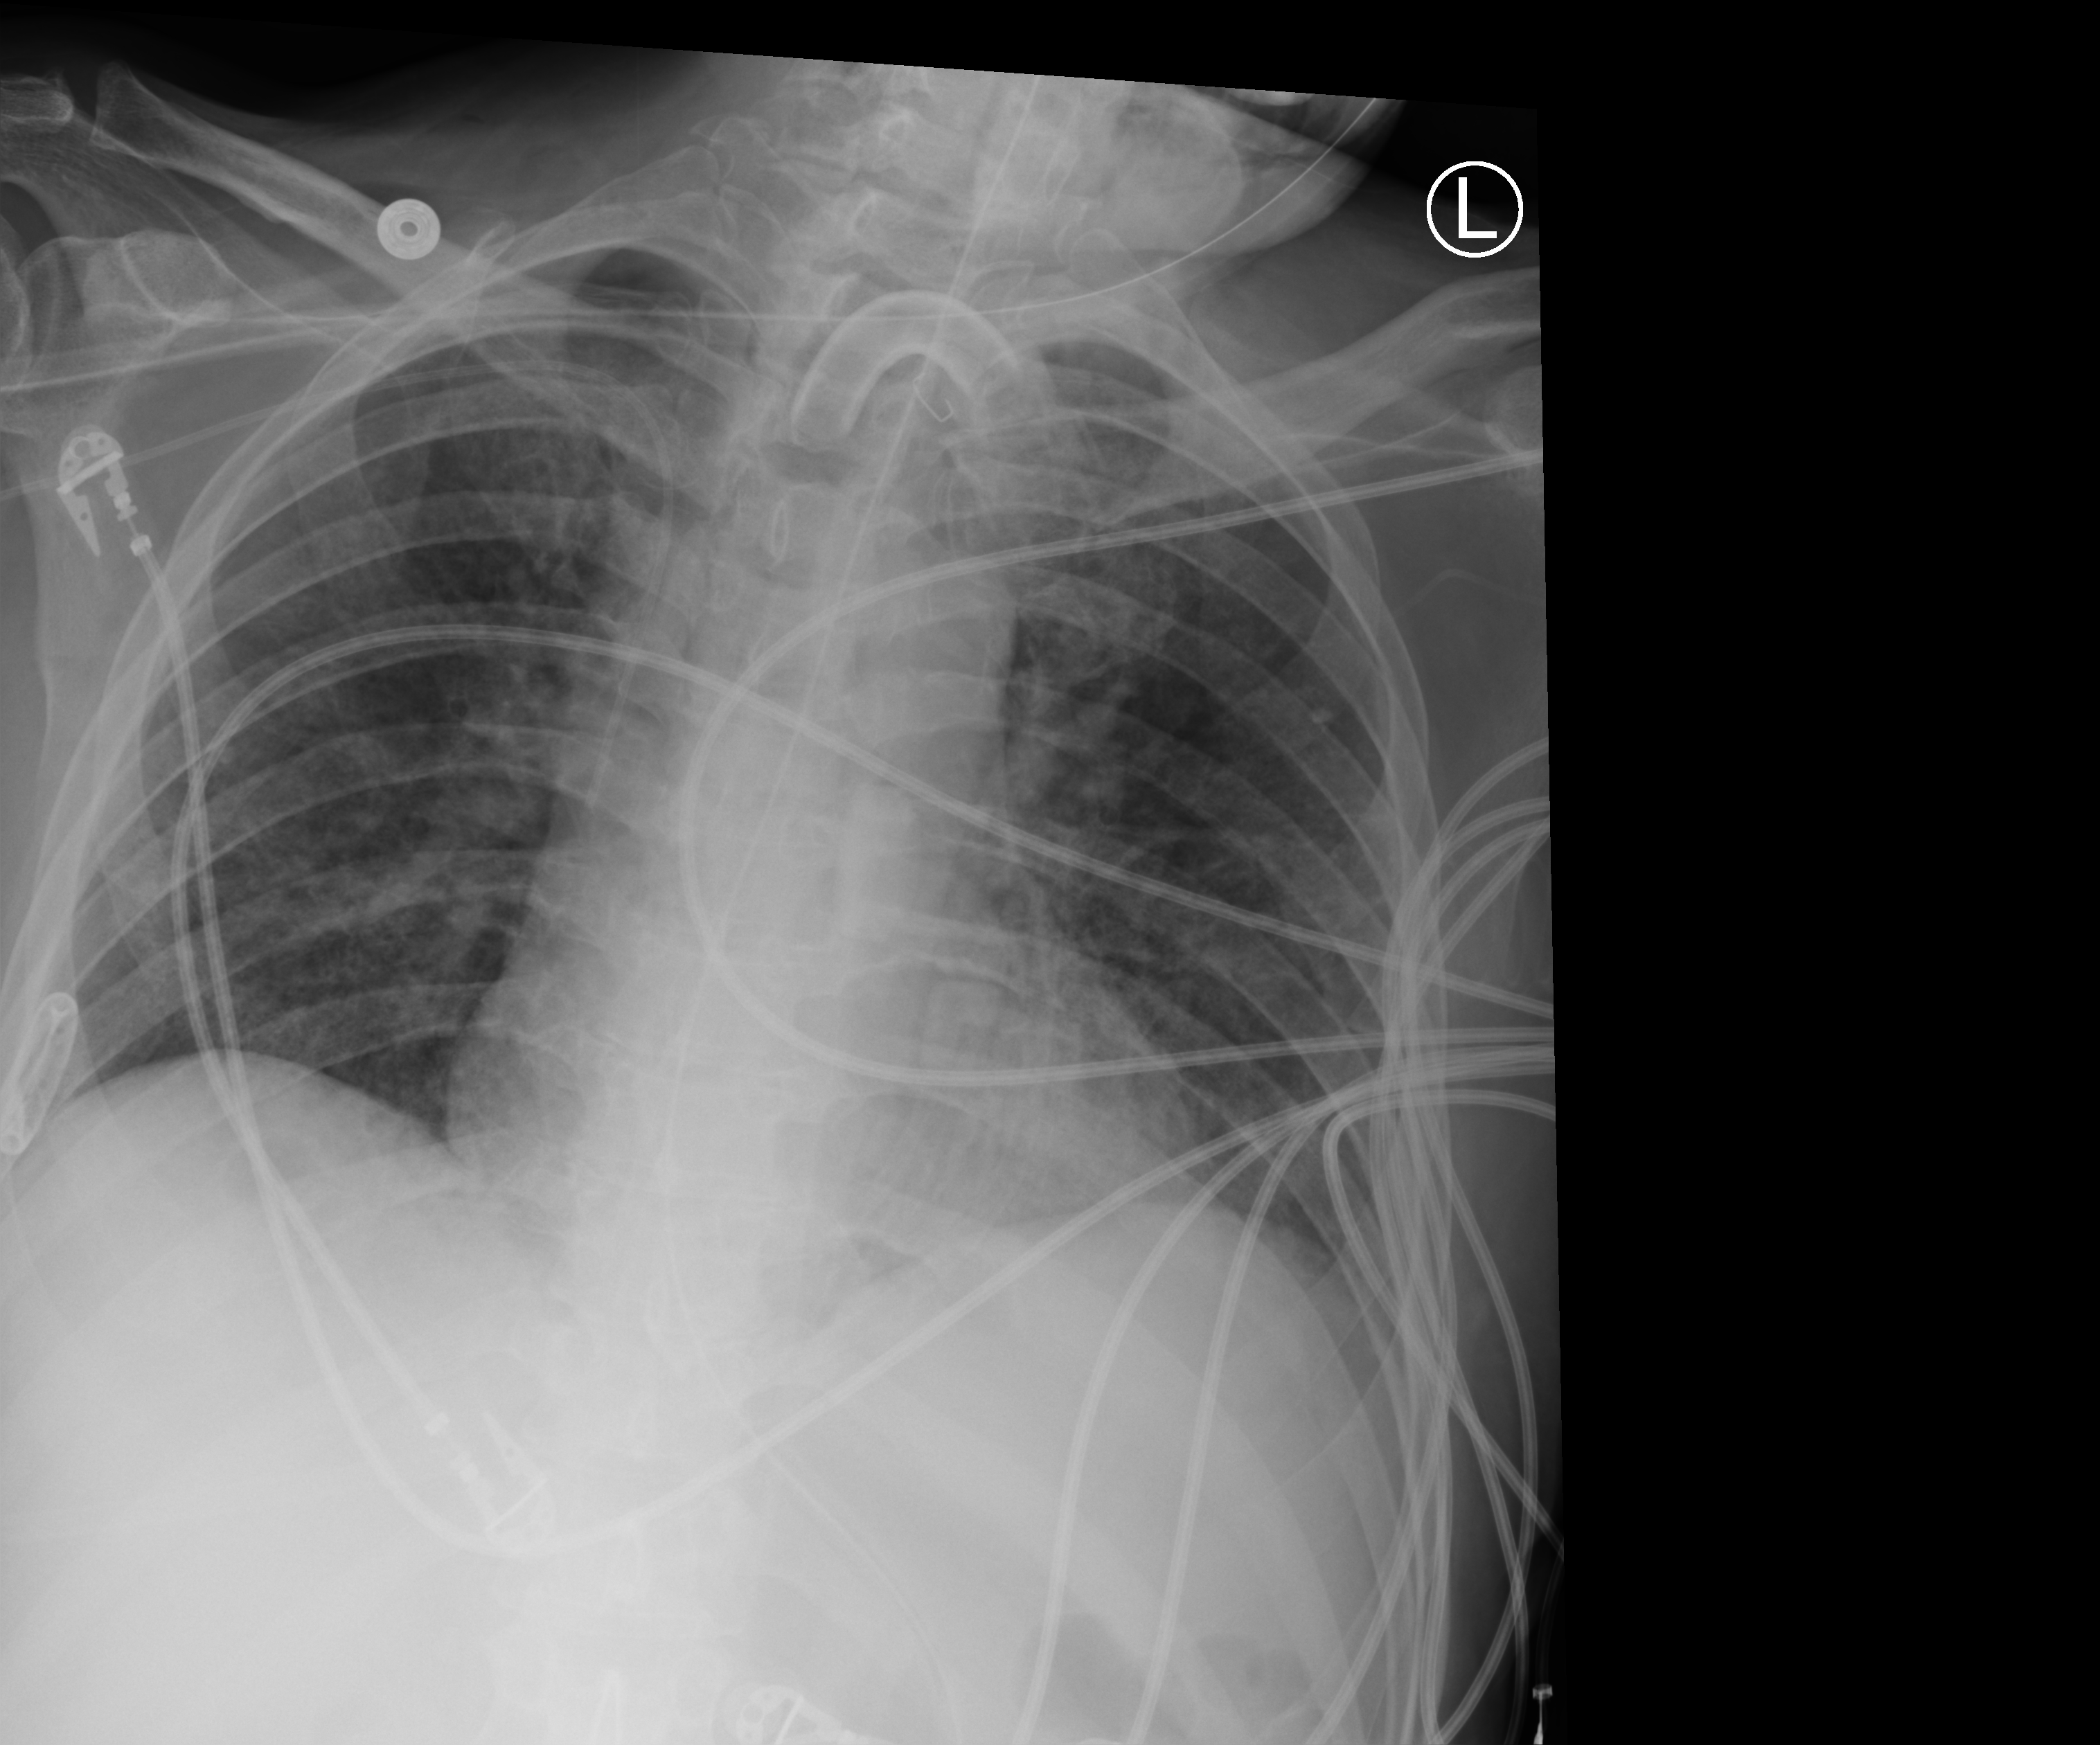
Portable chest radiograph; anteroposterior (AP) projection. Patient hospitalised with COVID-19; male, aged 18–59 years.
Admission-level facts for this patient (not findings on this image; timing relative to this image not recorded):
- mechanically ventilated during this hospital stay: yes
- admitted to intensive care during this hospital stay: yes